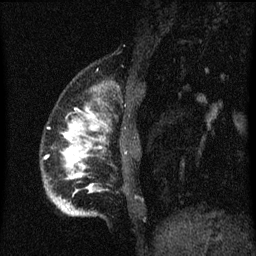
Breast MRI (dynamic contrast-enhanced), one sagittal slice; dynamic contrast-enhanced series, image 2 of 3 at this slice position (ordered by acquisition); 1.5 T; TE 4.2 ms, TR 8.4 ms; 2 mm slice thickness; 256 × 256 image matrix, field of view 180 × 180 mm. Patient: female, 34 years. Case-level facts recorded for this patient, not image findings: setting: breast cancer imaged before/during neoadjuvant chemotherapy; receptor status: HR-positive, HER2-negative.
Annotated regions visible in this slice (semi-automatically segmented with operator editing):
- analysis volume of interest (the breast-tissue region the enhancement analysis was run in; not a lesion): bounding box <42,80,143,217> (left, top, right, bottom; pixels)
- tumour enhancement mask (voxels above the 70 % enhancement threshold inside the analysis volume of interest): <62,108,99,193>